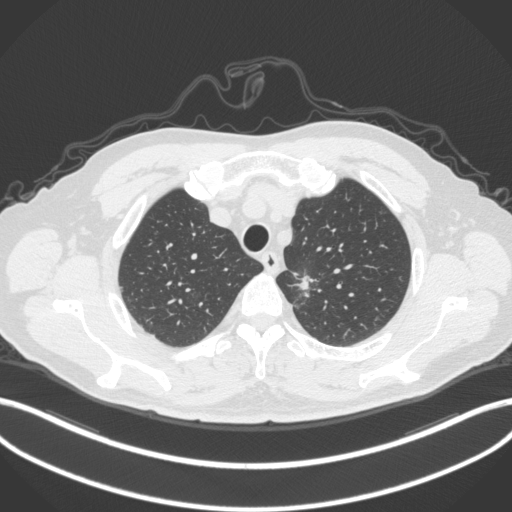
Chest CT, one axial slice. Slice 308 of 382 in the series (ordered by position). Reconstruction kernel B31f. 120 kVp. Lung window (W 1500 / L -600 HU). 1 mm slice thickness. 512 × 512 image matrix, field of view 400 × 400 mm. Patient: male, 64 years. From the clinical record (not read from this slice): clinical TNM (as recorded): T1c N0 M0.
Annotated regions visible in this slice (bounding box drawn by a radiologist):
- lung tumour (recorded histology: adenocarcinoma): bounding box <290,268,323,307> (left, top, right, bottom; pixels)